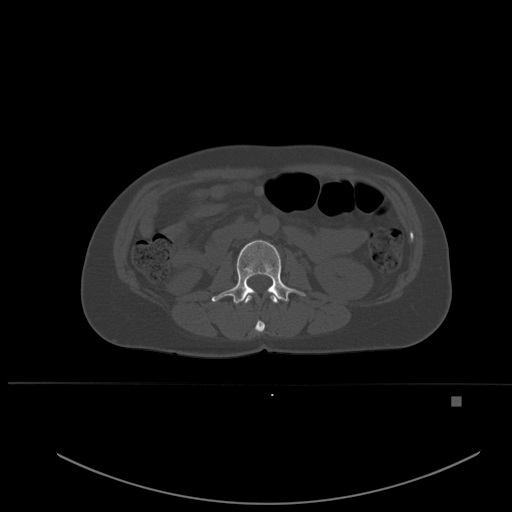
CT including the spine, one axial slice. Slice 217 of 651 in the series (ordered by position). Bone window (W 1800 / L 400 HU). 1.5 mm slice thickness. 512 × 512 image matrix, field of view 443 × 443 mm. Female patient, age 49 years. From the clinical record (not read from this slice): primary cancer: breast.
Structures marked on this image (semi-automatic segmentation, software-assisted and operator-edited):
- L1 vertebra: box from (x=244, y=295) to (x=278, y=332) px
- L2 vertebra: (x=212, y=240)–(x=305, y=304)